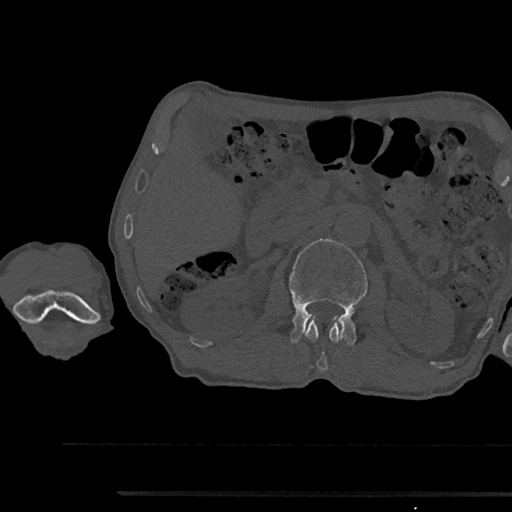
CT including the spine, one axial slice. Position 595 of 797 along the scan axis. Reconstruction kernel Br40s/3. Bone window (W 1800 / L 400 HU). 0.5 mm slice thickness. 512 × 512 image matrix, field of view 367 × 367 mm. Patient: male, 79 years. From the clinical record (not read from this slice): primary cancer: prostate.
Annotated regions visible in this slice (semi-automatically segmented with operator editing):
- L1 vertebra: box from (x=305, y=319) to (x=343, y=370) px
- L2 vertebra: (x=289, y=239)–(x=367, y=345)